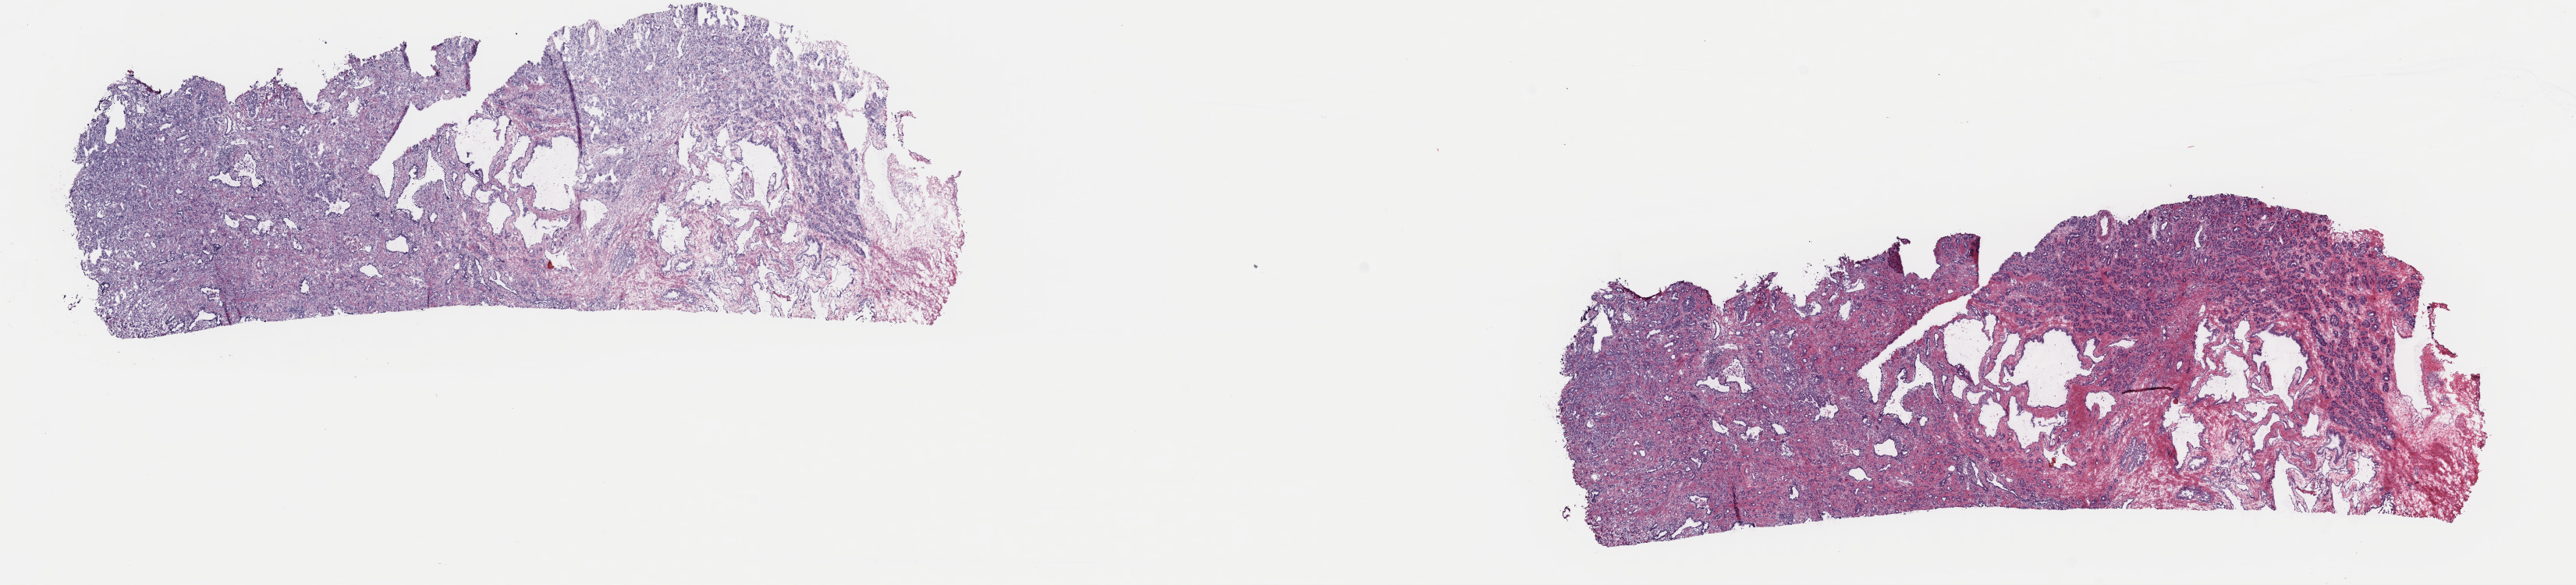
Digitized H&E-stained tissue section (whole slide), shown as a low-resolution overview of the whole scanned area (about 26.1 x 5.9 mm, from a 40x scan); frozen section from the top of the tissue portion; prostate, primary tumour sample. Male patient; age at initial diagnosis 68 years. Gleason score: 7 (4+3). Slide review estimates, as recorded: tumour cells 60%, tumour nuclei 65%, normal cells 40%, stromal cells 0%, necrosis 0%. Inflammatory infiltration, as recorded: lymphocyte infiltration 1%, monocyte infiltration 0%, neutrophil infiltration 0%.
Diagnosis: Adenocarcinoma, NOS (prostate gland).